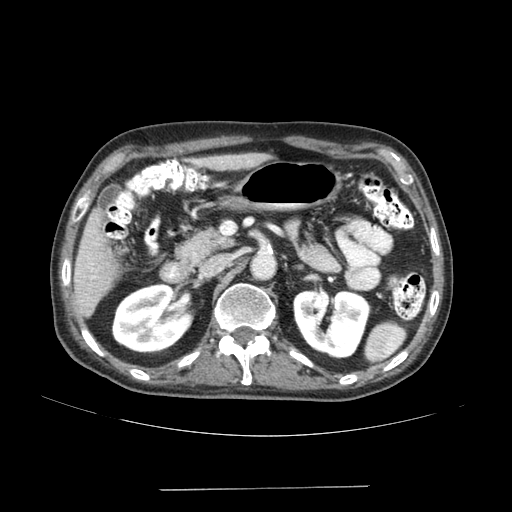
Contrast-enhanced abdominal CT (liver protocol), one axial slice. Slice 70 of 192 in the series (ordered by position). Reconstruction kernel SOFT. Soft-tissue window (W 400 / L 40 HU). 2.5 mm slice thickness. 512 × 512 image matrix, field of view 400 × 400 mm. From the clinical record (not read from this slice): diagnosis: hepatocellular carcinoma (patient treated with transarterial chemoembolisation; whether this scan precedes or follows treatment is not stated here); TNM stage (as recorded): Stage-IVA; Child-Pugh class: A; tumour differentiation: poorly differentiated; tumour nodularity: uninodular.
Structures marked on this image (semi-automatic segmentation, software-assisted and operator-edited):
- liver parenchyma outside the tumour (the mass and vessels are separate outlines, so this box may not span the whole liver): bounding box <74,153,268,316> (left, top, right, bottom; pixels)